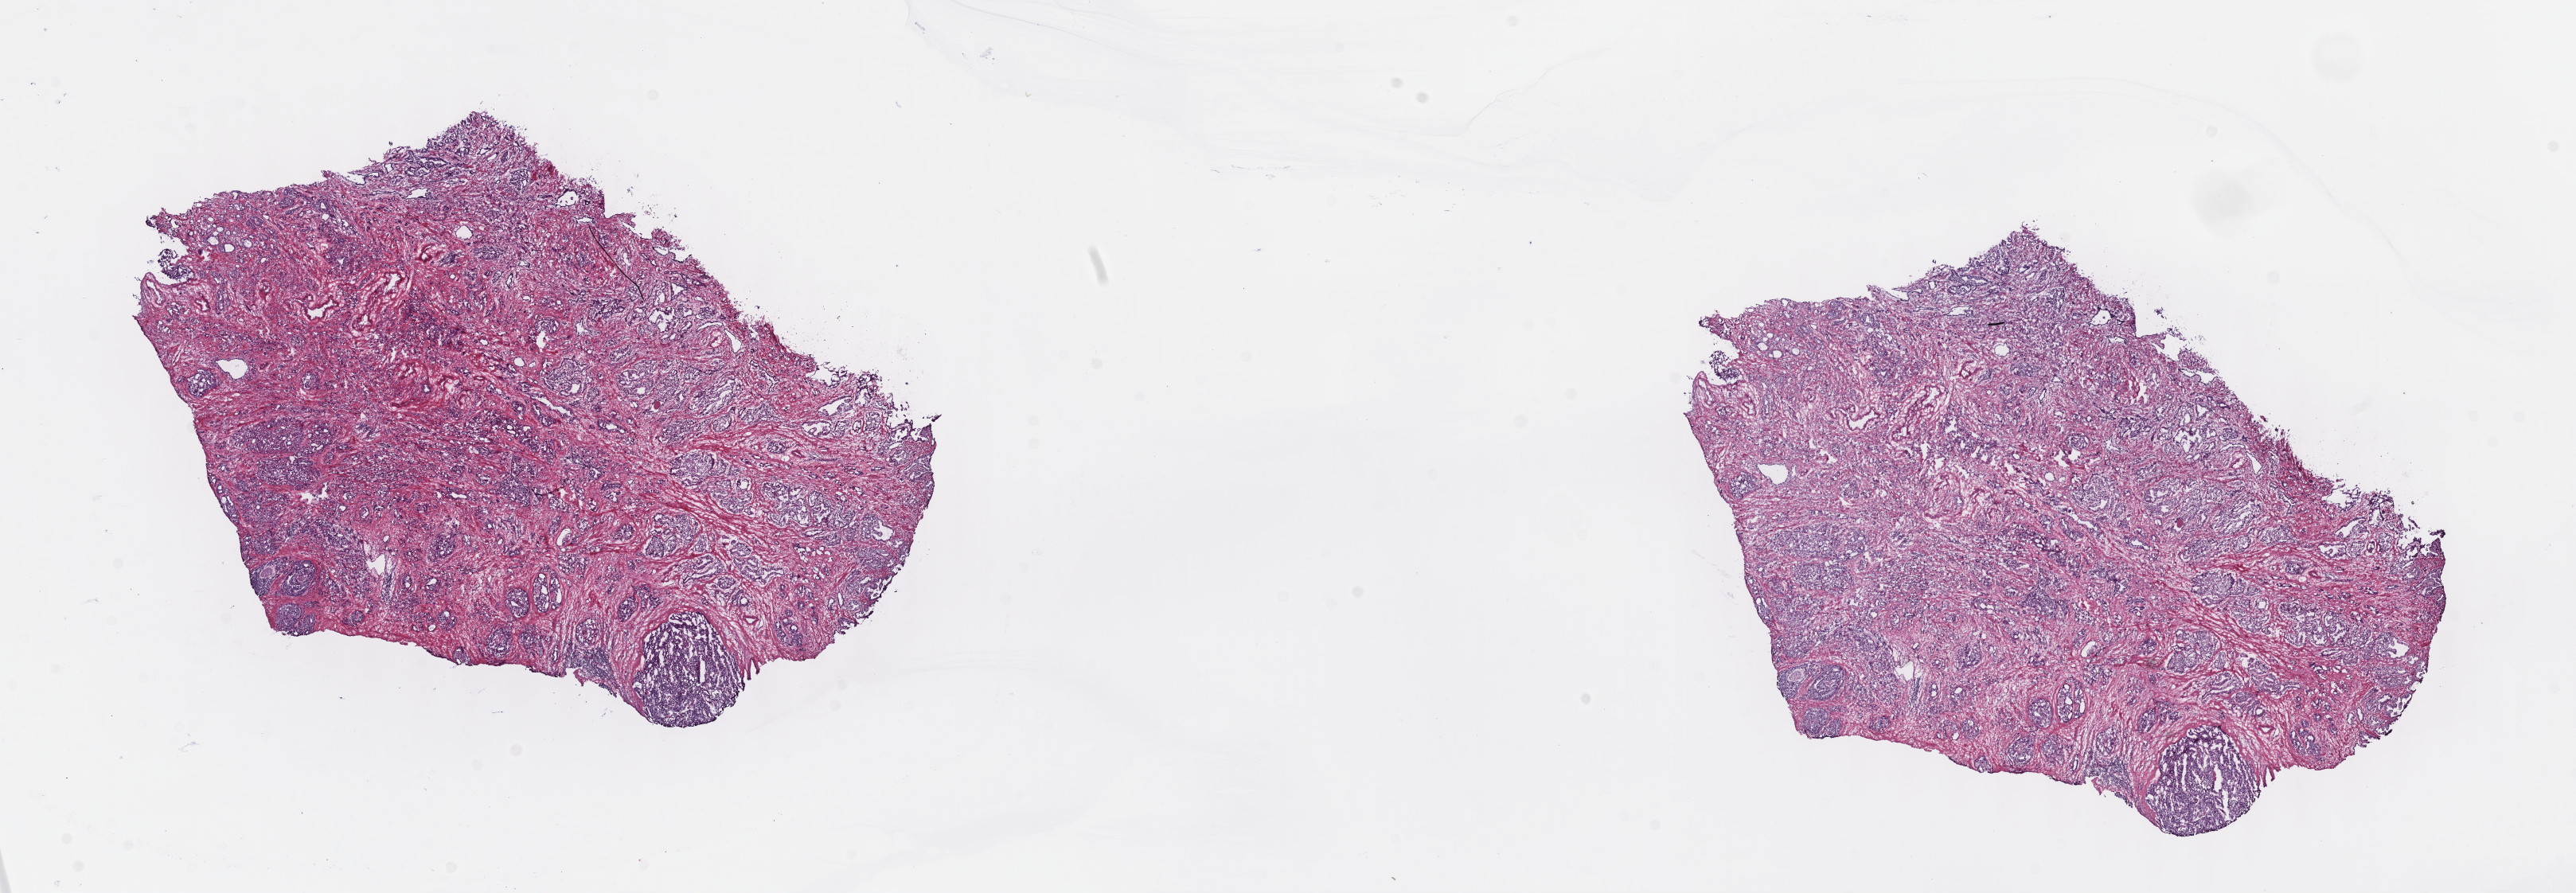
Whole-slide histology image, H&E-stained, shown as a low-resolution overview of the whole scanned area (about 26.2 x 9.1 mm, acquisition: 40x scan); frozen section; primary tumour sample from the prostate. Male patient; age at initial diagnosis 54 years. Gleason score: 9 (4+5). Composition of this section per pathologist review: tumour cells 50%, tumour nuclei 60%, normal cells 50%, stromal cells 0%, necrosis 0%. Infiltration values recorded for this section: lymphocyte infiltration 0%, monocyte infiltration 0%, neutrophil infiltration 0%.
* histologic diagnosis: Adenocarcinoma, NOS (prostate gland)
* laterality: bilateral